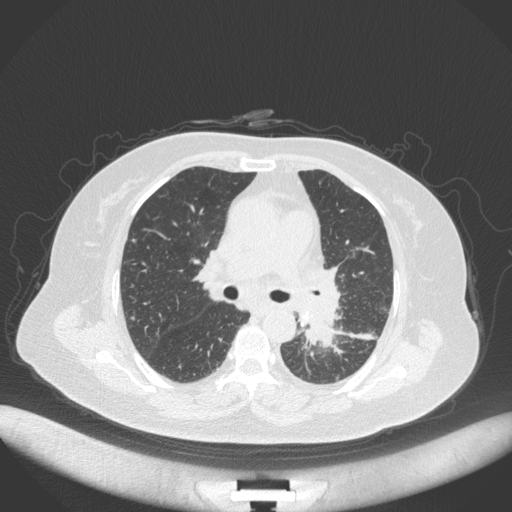
Chest CT, one axial slice. Position 208 of 328 along the scan axis. Reconstruction kernel B31f. 120 kVp. Lung window (W 1500 / L -600 HU). 1 mm slice thickness. 512 × 512 image matrix, field of view 400 × 400 mm. Female patient, age 69 years. Case-level facts recorded for this patient, not image findings: clinical TNM (as recorded): T2b N3 M1.
Structures marked on this image (rectangle marked by the reading radiologist):
- lung tumour (recorded histology: adenocarcinoma): bounding box (x1, y1, x2, y2) in pixels: (295, 306, 340, 349)